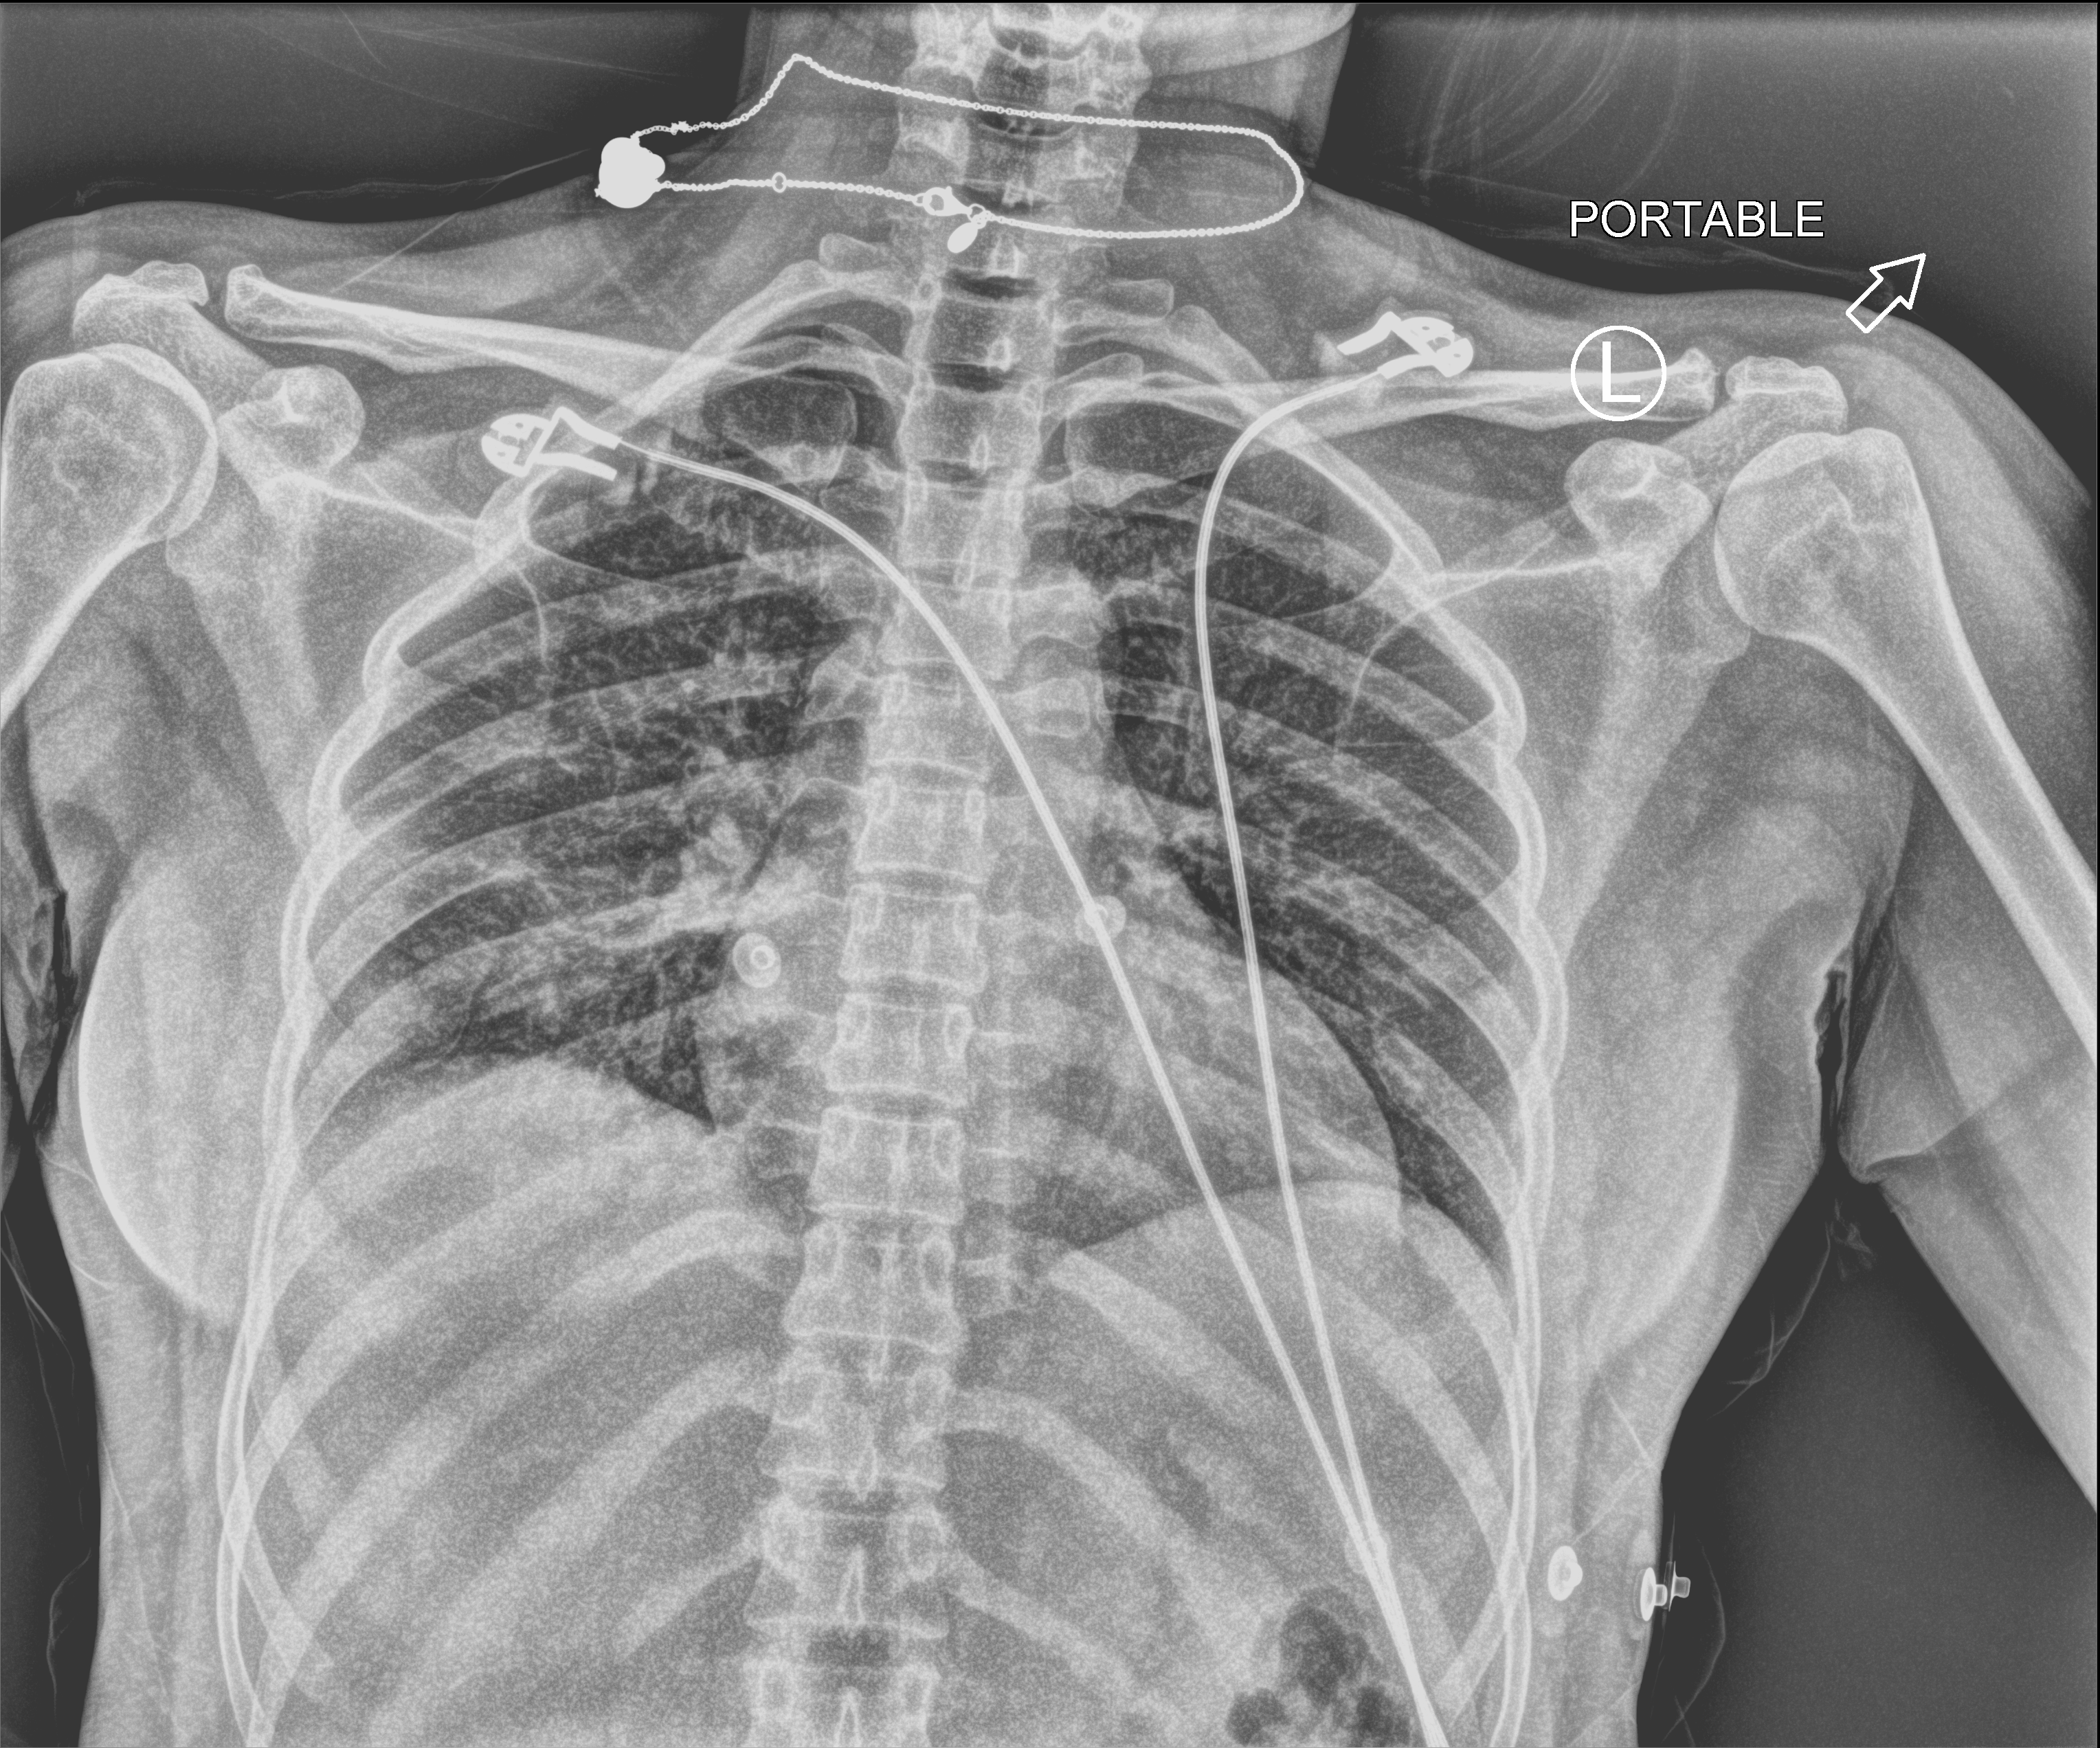
Chest X-ray (portable), anteroposterior (AP) projection. Female patient hospitalised with COVID-19, age 18–59 years.
Hospital-stay facts (about this admission, not read from this image; timing relative to this image not recorded): mechanically ventilated during this hospital stay: no; admitted to intensive care during this hospital stay: no.